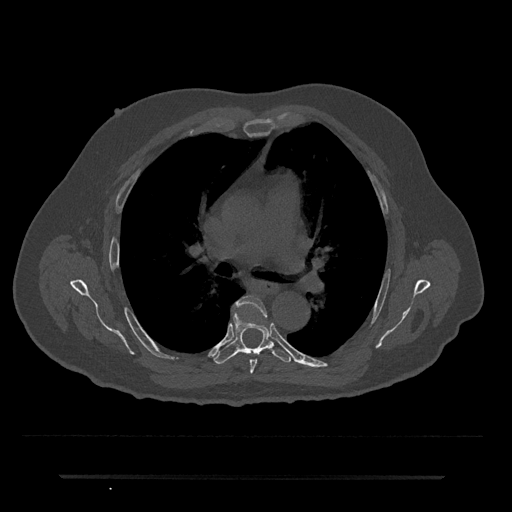
CT including the spine, one axial slice. Slice 454 of 797 in the series (ordered by position). 120 kVp. Bone window (W 1800 / L 400 HU). 512 × 512 image matrix, field of view 437 × 437 mm. Male patient, age 69 years. From the clinical record (not read from this slice): primary cancer: prostate.
Outlined on this slice (semi-automatic segmentation, software-assisted and operator-edited):
- T5 vertebra: bounding box (x1, y1, x2, y2) in pixels: (233, 295, 267, 374)
- T6 vertebra: (214, 311, 292, 364)